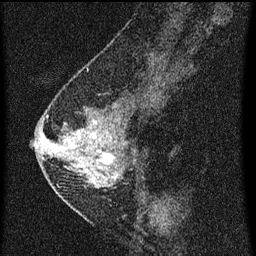
Breast MRI (dynamic contrast-enhanced), one sagittal slice. Position 25 of 60 along the scan axis. Dynamic contrast-enhanced series, image 2 of 3 at this slice position (ordered by acquisition). 1.5 T. TE 4.2 ms, TR 8 ms. 256 × 256 image matrix, field of view 180 × 180 mm. Patient: female, 47 years.
Structures marked on this image (semi-automatically segmented with operator editing):
- analysis volume of interest (the breast-tissue region the enhancement analysis was run in; not a lesion): box from (x=42, y=92) to (x=140, y=199) px
- tumour enhancement mask (voxels above the 70 % enhancement threshold inside the analysis volume of interest): (x=42, y=122)–(x=115, y=187)